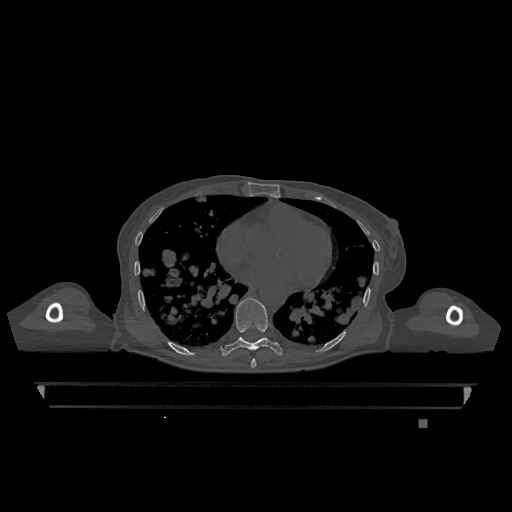
CT including the spine, one axial slice; bone window (W 1800 / L 400 HU); 512 × 512 image matrix, field of view 500 × 500 mm. Female patient, age 74 years. From the clinical record (not read from this slice): primary cancer: lung.
Structures marked on this image (semi-automatically segmented with operator editing):
- T7 vertebra: bounding box <251,358,257,368> (left, top, right, bottom; pixels)
- T9 vertebra: <222,298,283,357>